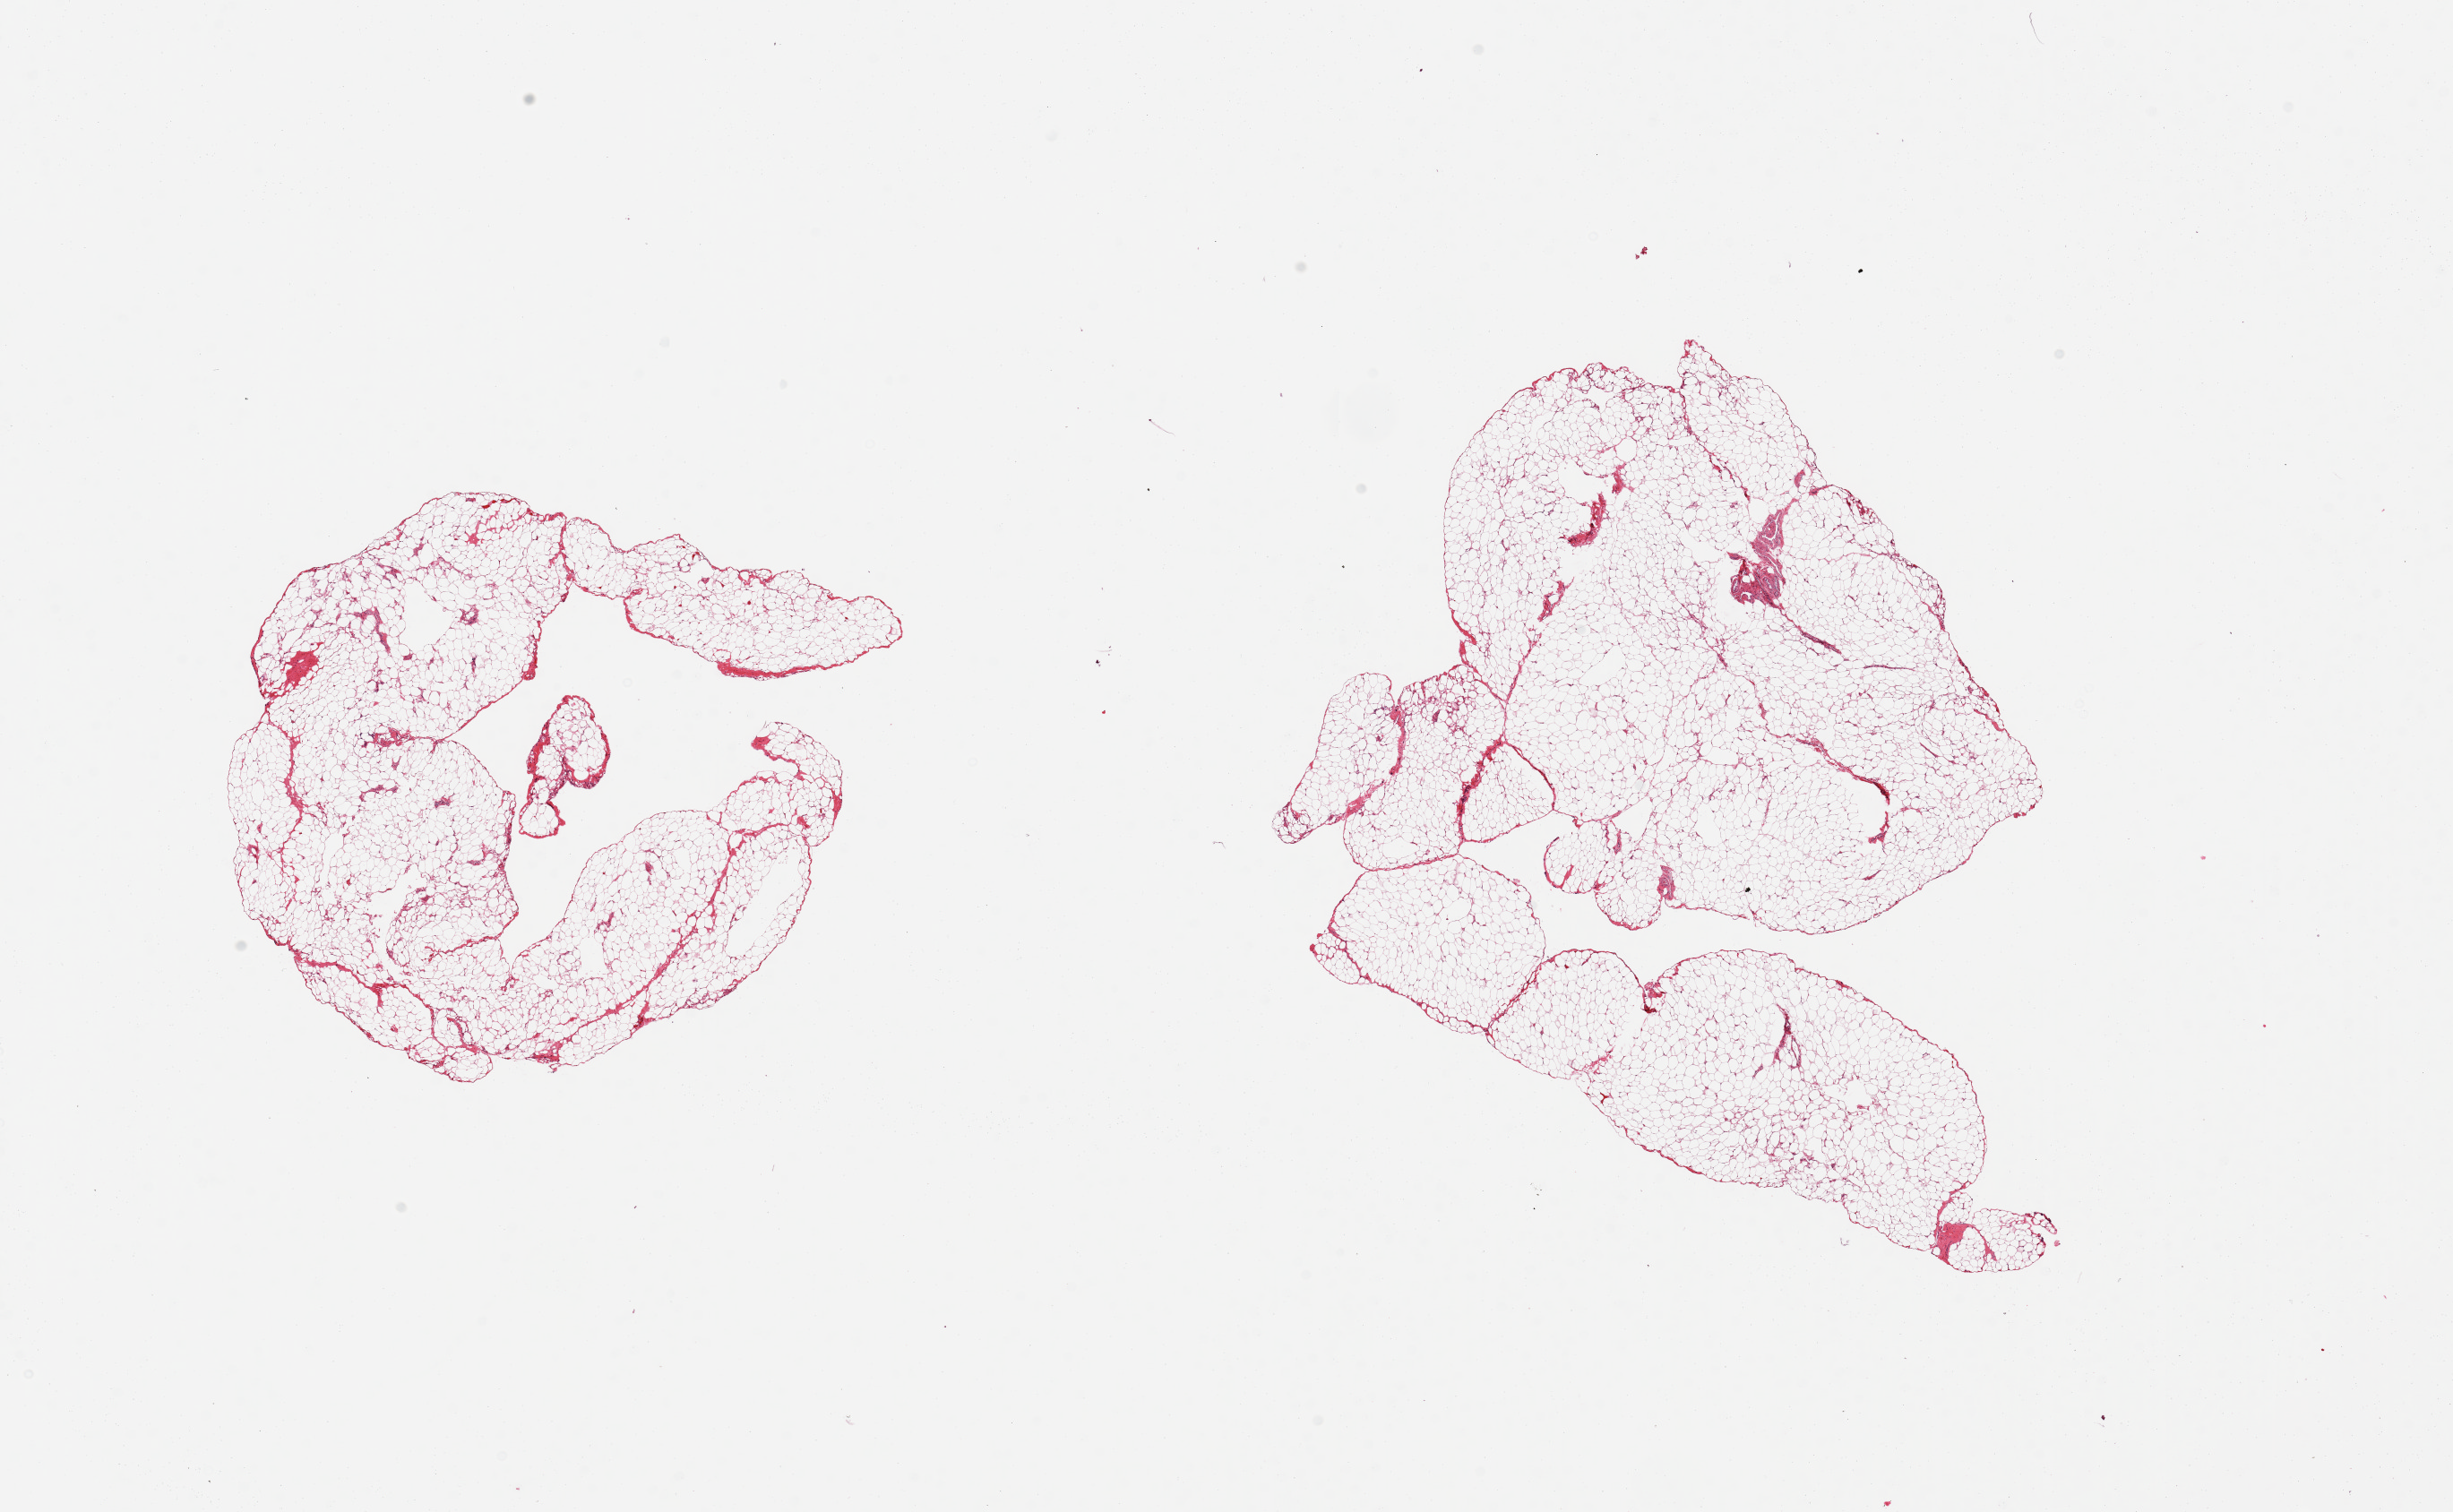
Whole-slide image, hematoxylin and eosin (H&E) stain, brightfield, a low-resolution overview of the entire scanned area, about 21.7 x 13.4 mm (from a 20x scan), PAXgene-fixed paraffin-embedded (PFPE) section, section of omentum (target tissue), tissue donor sample.
Reviewer comment on this tissue sample: 2 pieces.